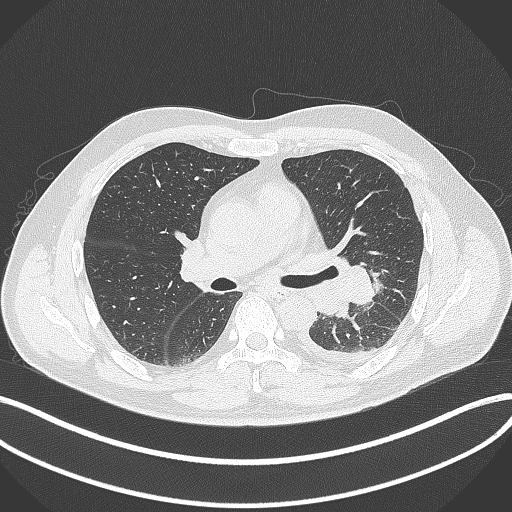
Chest CT, one axial slice. Reconstruction kernel B70f. 120 kVp. Lung window (W 1500 / L -600 HU). 1 mm slice thickness. 512 × 512 image matrix, field of view 400 × 400 mm. Male patient, age 58 years. Case-level facts recorded for this patient, not image findings: clinical TNM (as recorded): T3 N1 M1b.
Annotated regions visible in this slice (bounding box drawn by a radiologist):
- lung tumour (recorded histology: small cell carcinoma): box from (x=348, y=258) to (x=380, y=308) px